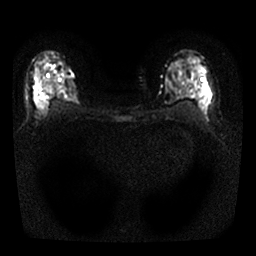
Breast MRI, one axial slice; position 17 of 25 along the scan axis; diffusion-weighted series; image 2 of 4 stored at this slice position (different b-values; order by instance number); 1.5 T; 4 mm slice thickness; 256 × 256 image matrix. Female patient.
Annotated regions visible in this slice (outlined manually by an expert reader):
- tumour on diffusion-weighted imaging: bounding box (x1, y1, x2, y2) in pixels: (35, 83, 75, 107)